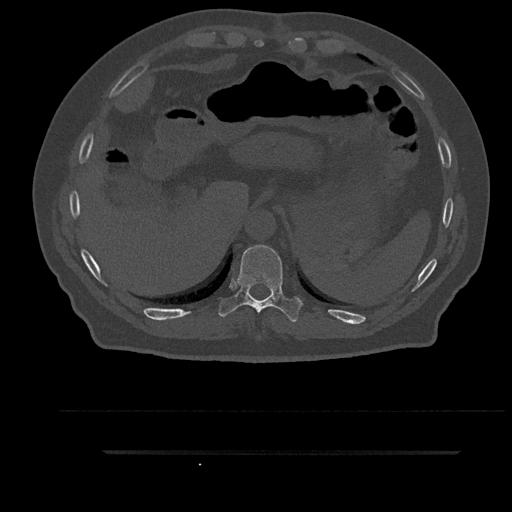
CT including the spine, one axial slice. Position 372 of 797 along the scan axis. 120 kVp. Bone window (W 1800 / L 400 HU). 0.5 mm slice thickness. 512 × 512 image matrix, field of view 432 × 432 mm. Male patient, age 63 years. From the clinical record (not read from this slice): primary cancer: renal.
Outlined on this slice (semi-automatic segmentation, software-assisted and operator-edited):
- T10 vertebra: bounding box [x1, y1, x2, y2] px = [218, 245, 303, 322]
- T9 vertebra: [265, 306, 268, 308]